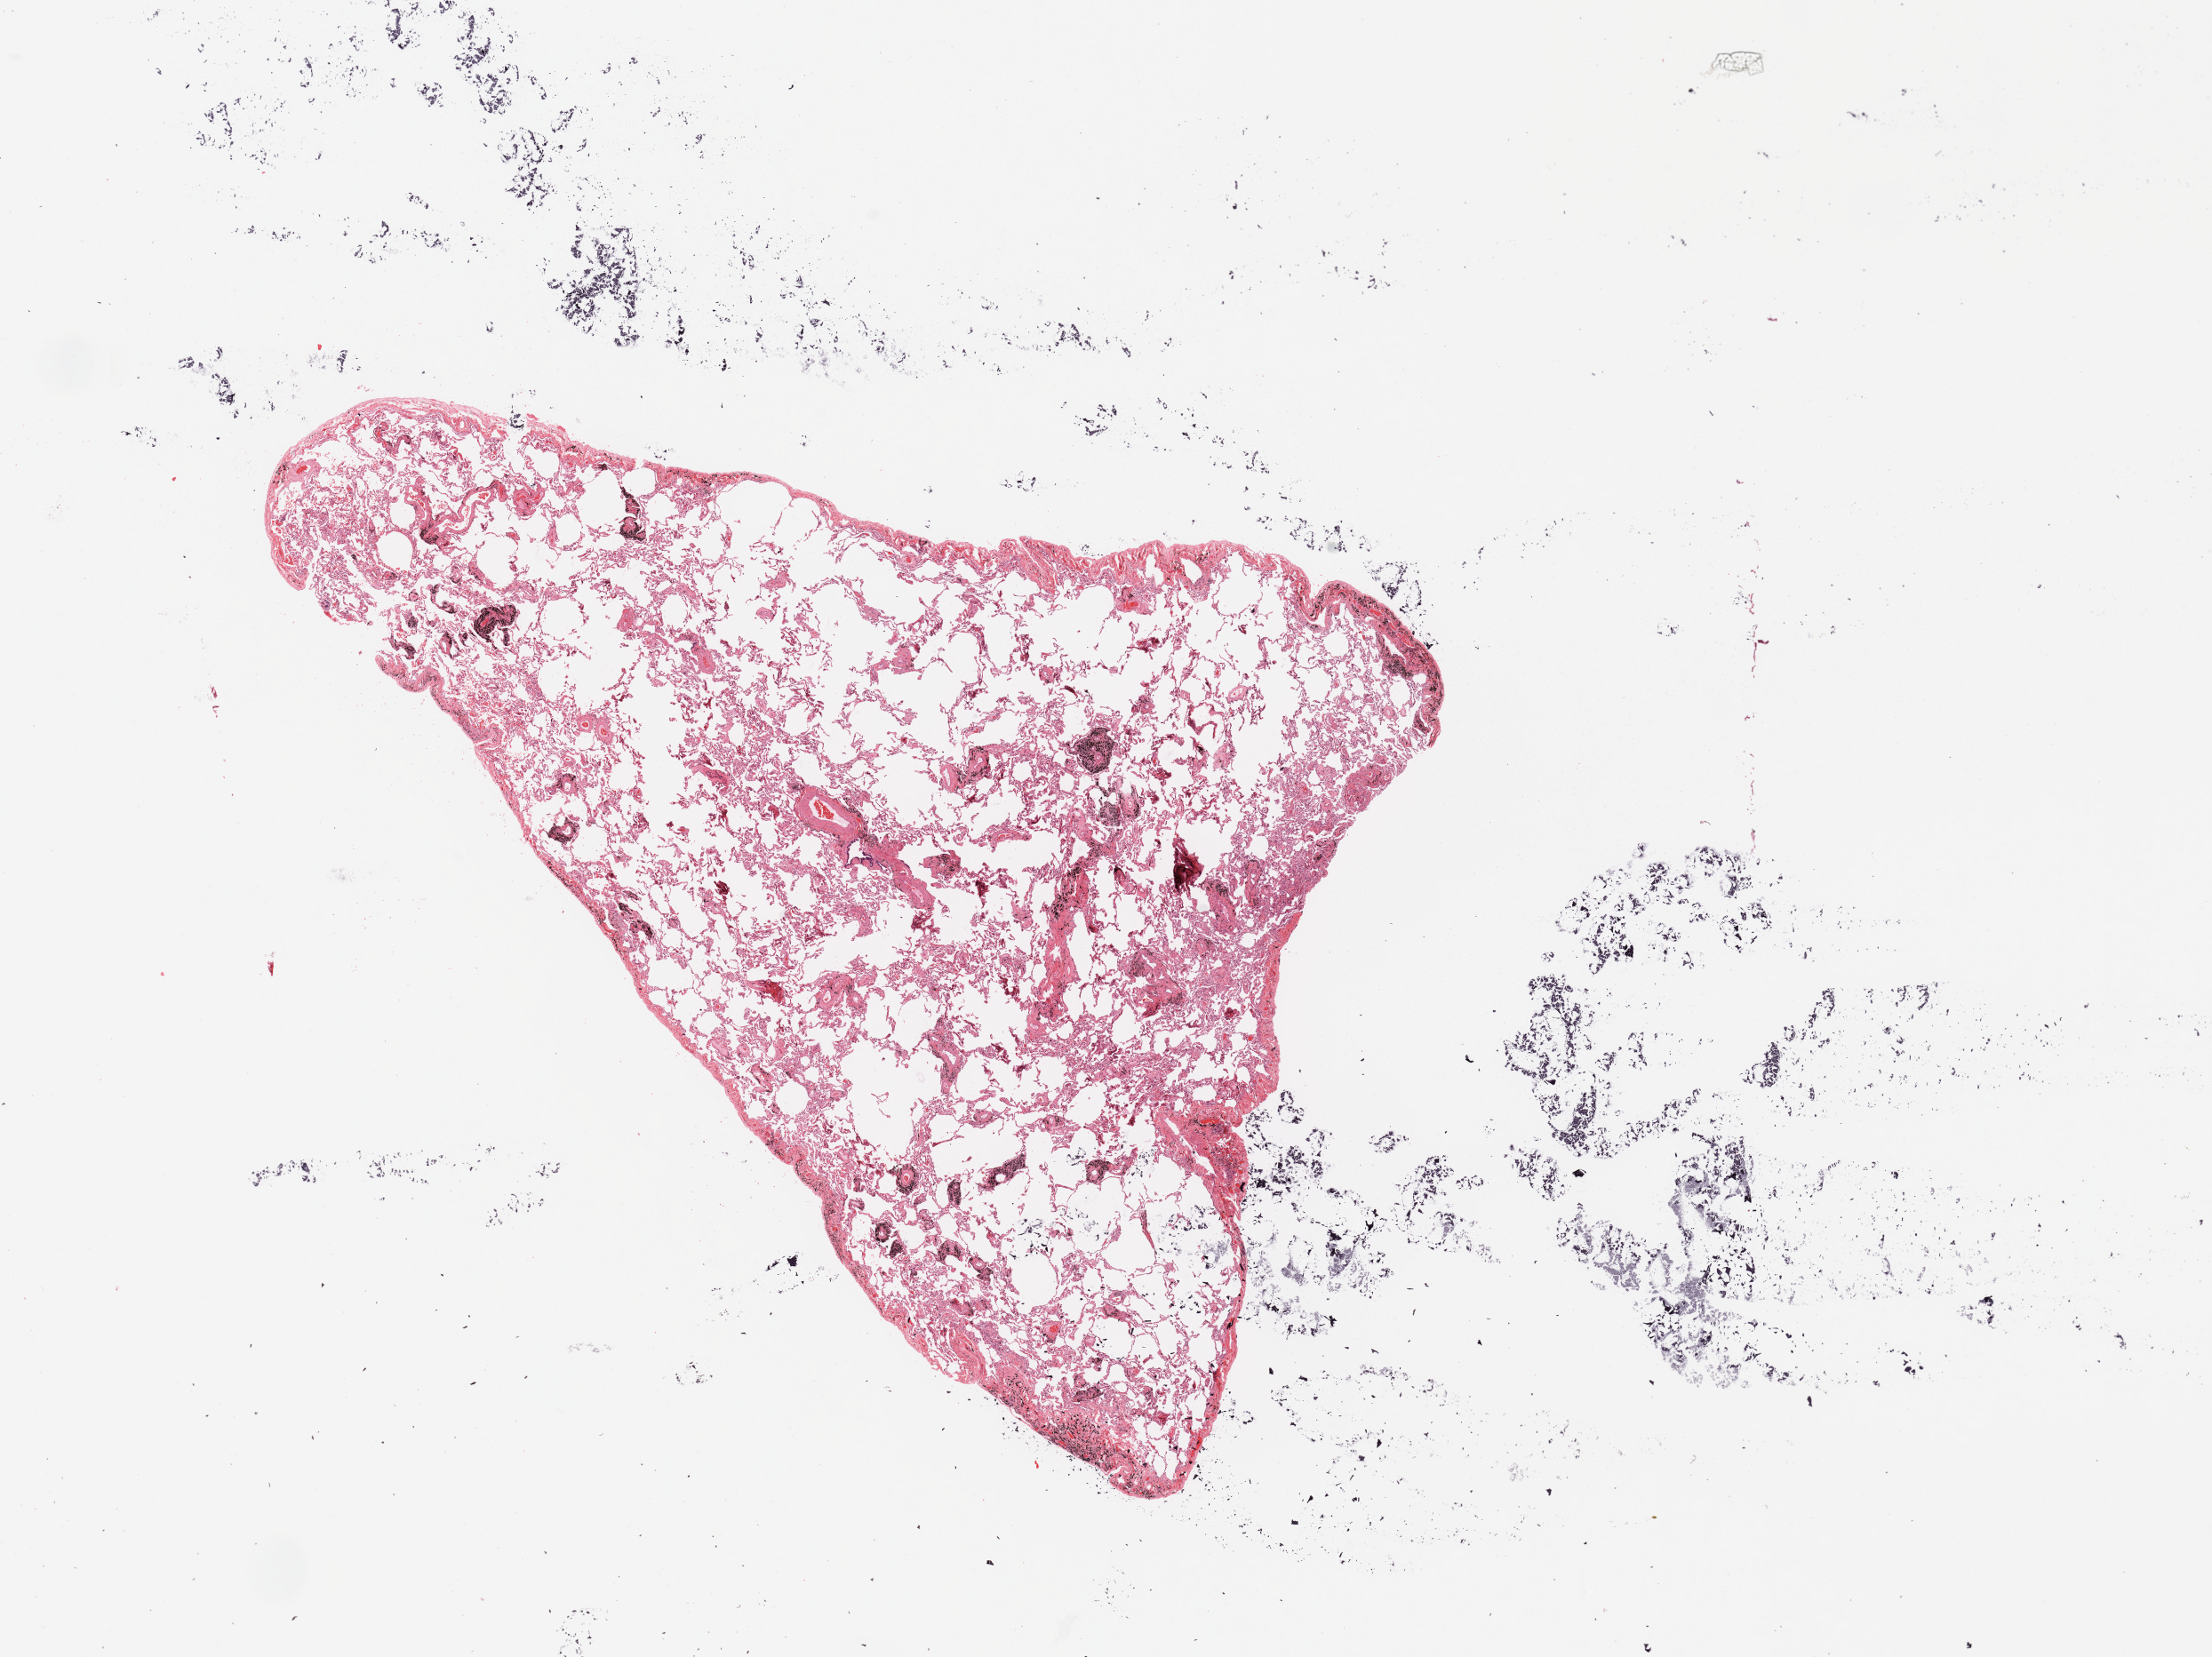
Whole-slide histology image, H&E — shown as a low-resolution overview of the whole scanned area (about 19.7 x 14.8 mm); normal (non-tumour) tissue sample, sampled site: lung. 69-year-old female patient.
This section: normal (non-tumour) tissue from the same patient. Patient diagnosis: Squamous cell carcinoma, NOS.